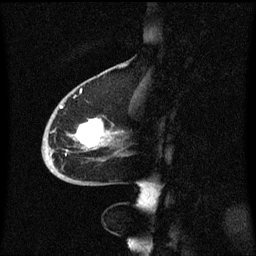
Breast MRI (dynamic contrast-enhanced), one sagittal slice; dynamic contrast-enhanced series, image 2 of 3 at this slice position (ordered by acquisition); 1.5 T; TE 4.2 ms, TR 8.4 ms; 256 × 256 image matrix, field of view 200 × 200 mm. Patient: female, 68 years. From the clinical record (not read from this slice): setting: breast cancer imaged before/during neoadjuvant chemotherapy; receptor status: triple-negative.
Annotated regions visible in this slice (semi-automatically segmented with operator editing):
- analysis volume of interest (the breast-tissue region the enhancement analysis was run in; not a lesion): bounding box <43,94,130,173> (left, top, right, bottom; pixels)
- tumour enhancement mask (voxels above the 70 % enhancement threshold inside the analysis volume of interest): <49,106,114,171>